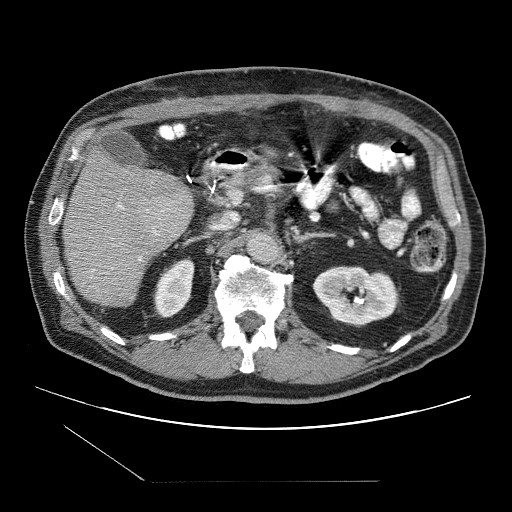
Contrast-enhanced abdominal CT (liver protocol), one axial slice; slice 44 of 109 in the series (ordered by position); reconstruction kernel STANDARD; one of 2 acquisitions stored at this slice position; soft-tissue window (W 400 / L 40 HU); 2.5 mm slice thickness; 512 × 512 image matrix, field of view 400 × 400 mm. Case-level facts recorded for this patient, not image findings: diagnosis: hepatocellular carcinoma (patient treated with transarterial chemoembolisation; whether this scan precedes or follows treatment is not stated here); TNM stage (as recorded): Stage-IIIB.
Structures marked on this image (semi-automatic segmentation, software-assisted and operator-edited):
- liver parenchyma outside the tumour (the mass and vessels are separate outlines, so this box may not span the whole liver): bounding box <62,150,194,306> (left, top, right, bottom; pixels)
- liver vessels: <92,204,157,273>